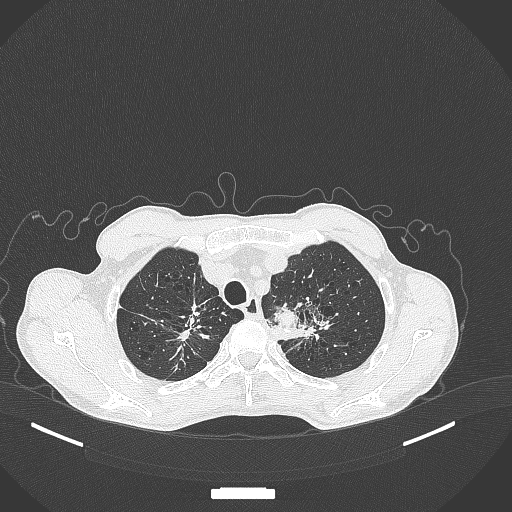
Chest CT, one axial slice. Position 362 of 386 along the scan axis. Reconstruction kernel B70f. Lung window (W 1500 / L -600 HU). 1 mm slice thickness. 512 × 512 image matrix. Male patient, age 65 years. From the clinical record (not read from this slice): clinical TNM (as recorded): T2b N0 M0; histopathological grade: G2.
Outlined on this slice (rectangle marked by the reading radiologist):
- lung tumour (recorded histology: adenocarcinoma): bounding box <266,299,305,330> (left, top, right, bottom; pixels)